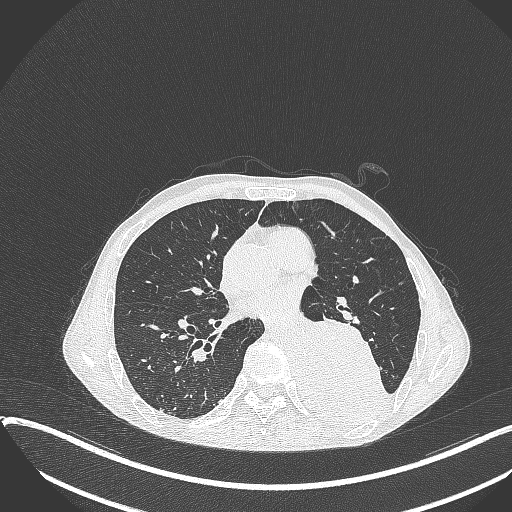
Chest CT, one axial slice. Position 174 of 401 along the scan axis. Reconstruction kernel B70f. 120 kVp. Lung window (W 1500 / L -600 HU). 512 × 512 image matrix, field of view 400 × 400 mm. Male patient, age 57 years. From the clinical record (not read from this slice): clinical TNM (as recorded): T4 N0 M0.
Outlined on this slice (rectangle marked by the reading radiologist):
- lung tumour (recorded histology: squamous cell carcinoma): bounding box <294,313,391,428> (left, top, right, bottom; pixels)